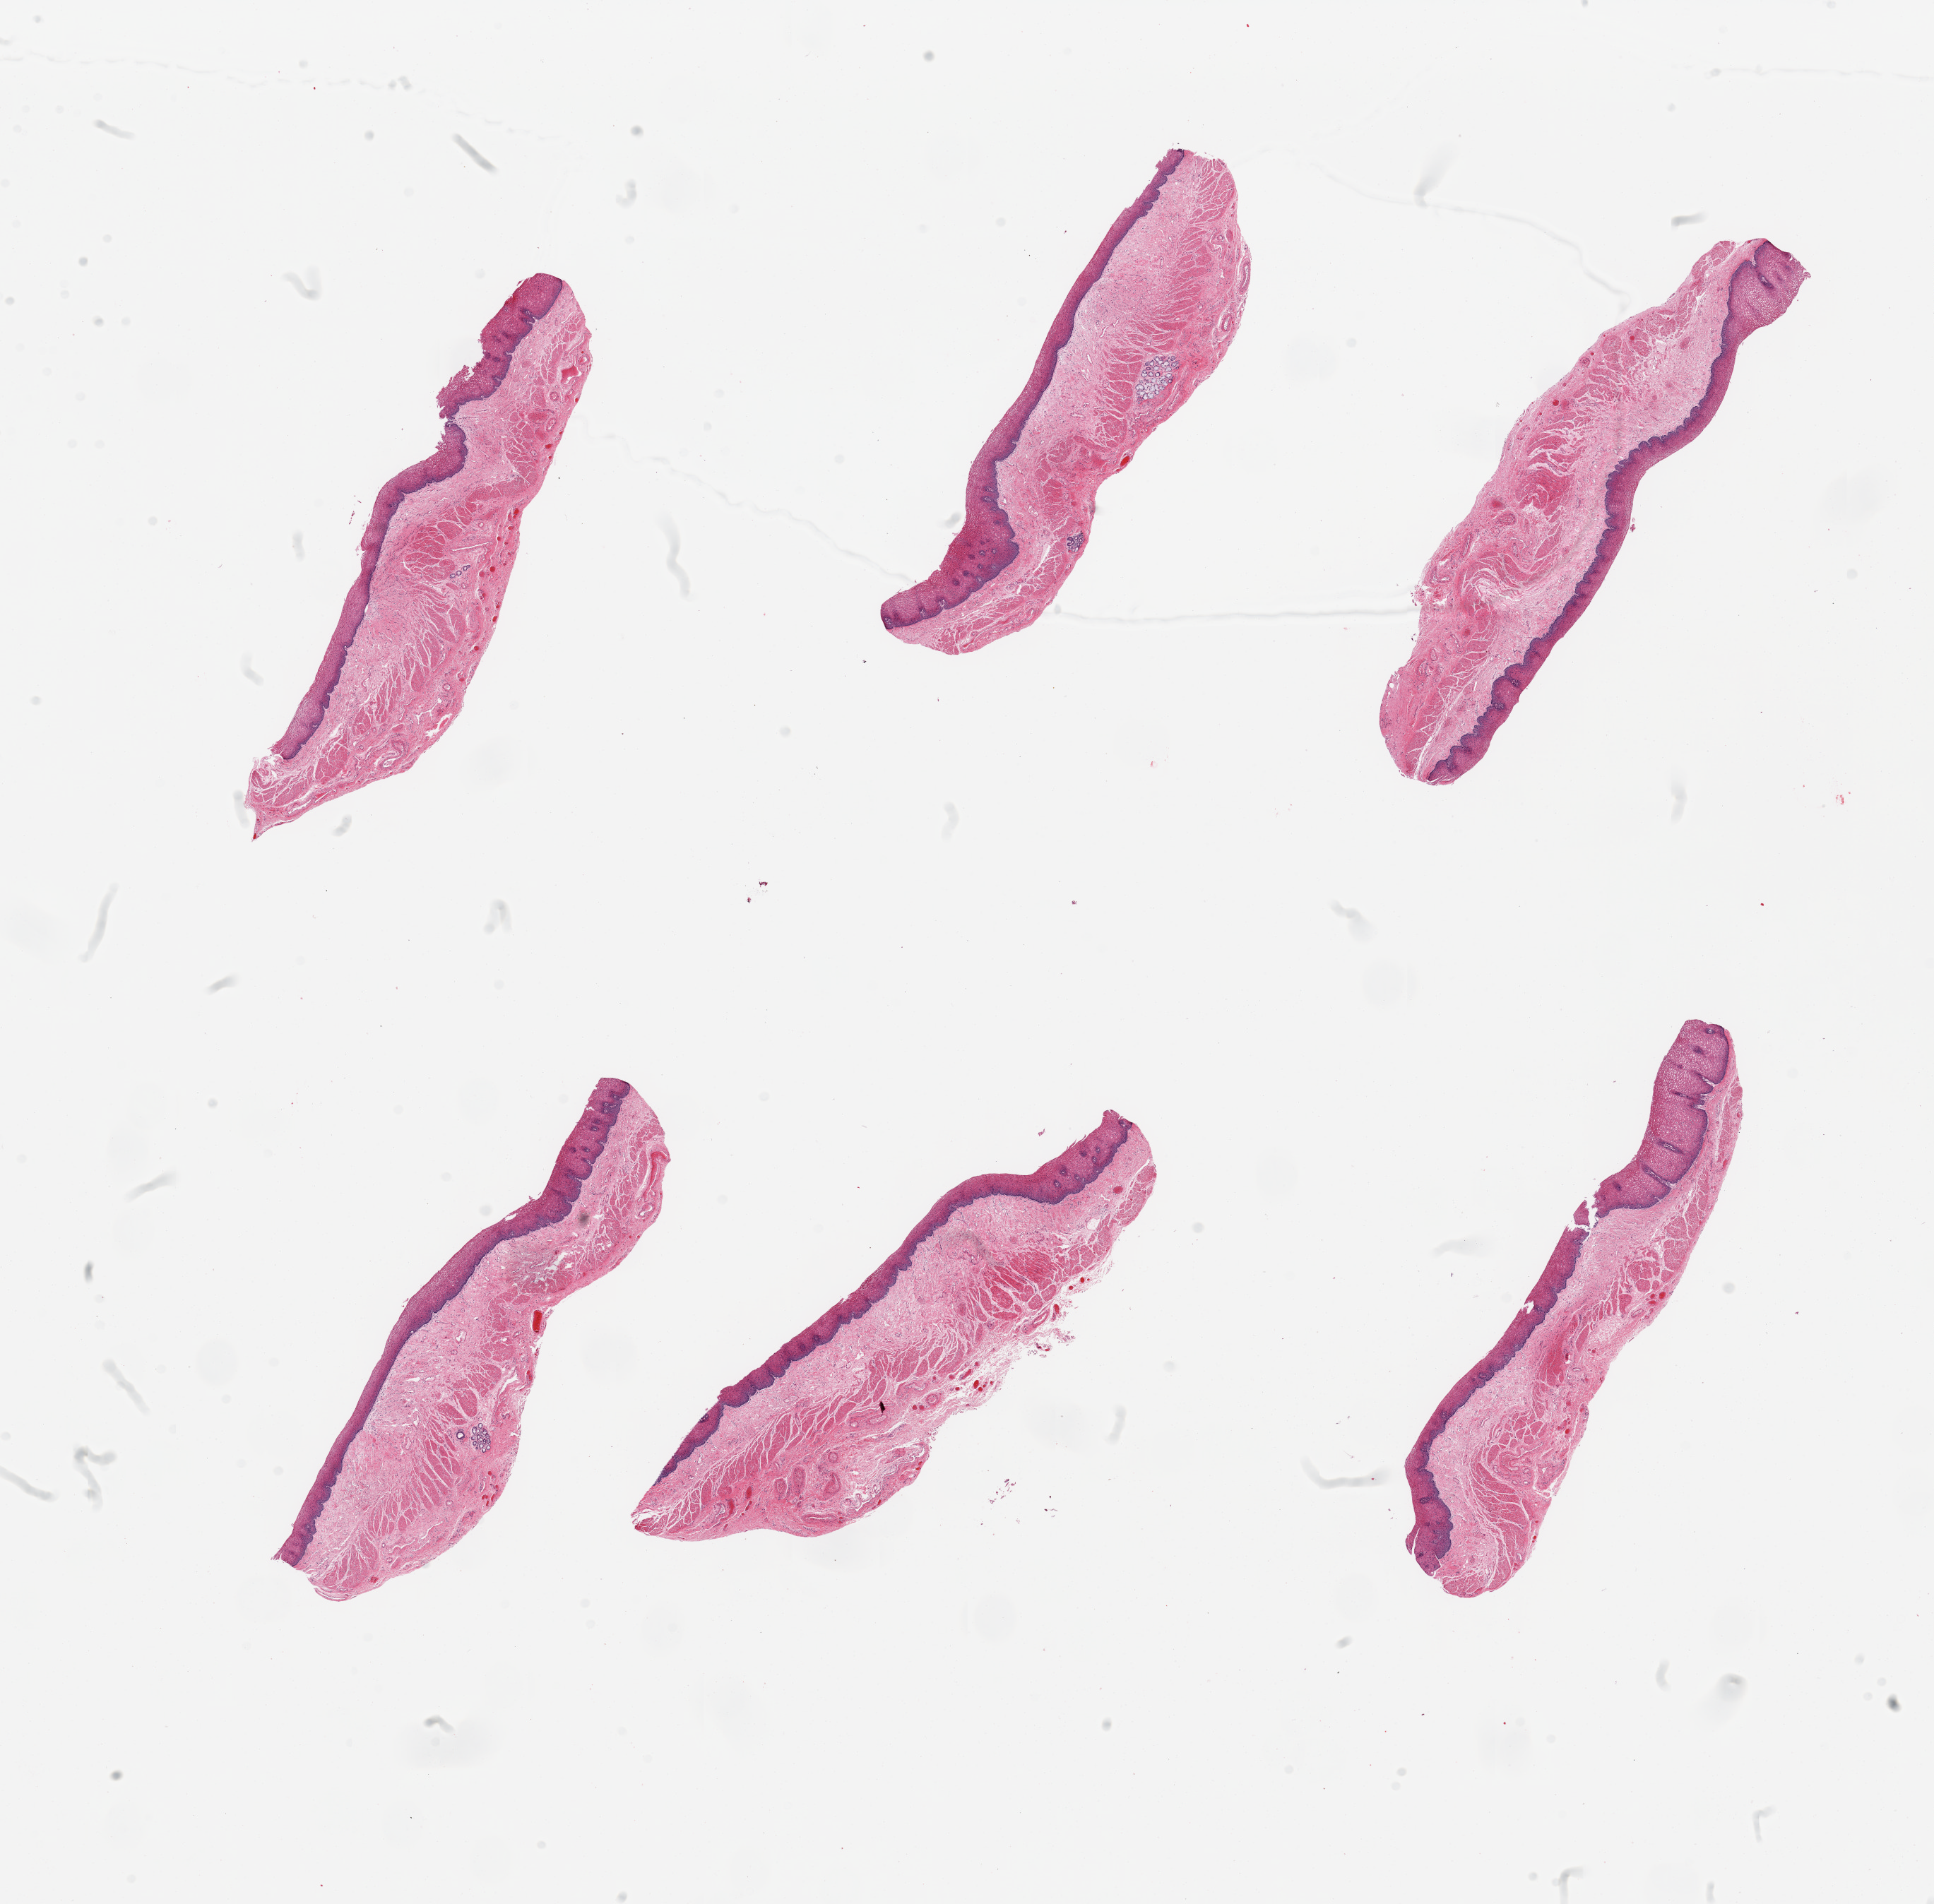
Whole-slide image, hematoxylin and eosin (H&E) stain, brightfield, a low-resolution overview of the entire scanned area, about 21.7 x 21.3 mm, PAXgene-fixed, paraffin-embedded tissue, target tissue: esophageal mucous membrane, donor tissue sample. Male donor.
- reviewer comment on this tissue sample: 6 pieces, squamous mucosa is ~1520% thickness; submucosal mucus glands noted